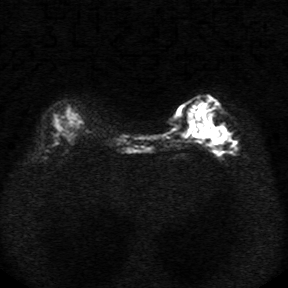
Breast MRI, one axial slice; slice 11 of 34 in the series (ordered by position); diffusion-weighted series; image 2 of 4 stored at this slice position (different b-values; order by instance number); 1.5 T; 5 mm slice thickness; 288 × 288 image matrix. Female patient.
Structures marked on this image (expert manual segmentation):
- tumour on diffusion-weighted imaging: bounding box <187,124,224,139> (left, top, right, bottom; pixels)